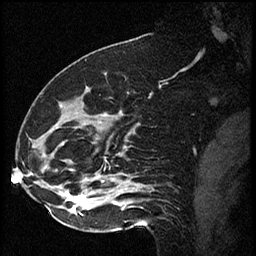
Breast MRI (dynamic contrast-enhanced), one sagittal slice; slice 24 of 60 in the series (ordered by position); dynamic contrast-enhanced series, image 2 of 2 at this slice position (ordered by acquisition); 1.5 T; TE 4.2 ms, TR 17.3 ms; 2 mm slice thickness; 256 × 256 image matrix, field of view 200 × 200 mm. Female patient. Case-level facts recorded for this patient, not image findings: setting: breast cancer imaged before/during neoadjuvant chemotherapy; receptor status: HR-positive, HER2-negative.
Structures marked on this image (semi-automatically segmented with operator editing):
- analysis volume of interest (the breast-tissue region the enhancement analysis was run in; not a lesion): bounding box (x1, y1, x2, y2) in pixels: (41, 93, 115, 223)
- tumour enhancement mask (voxels above the 100 % enhancement threshold inside the analysis volume of interest): (69, 196, 85, 213)